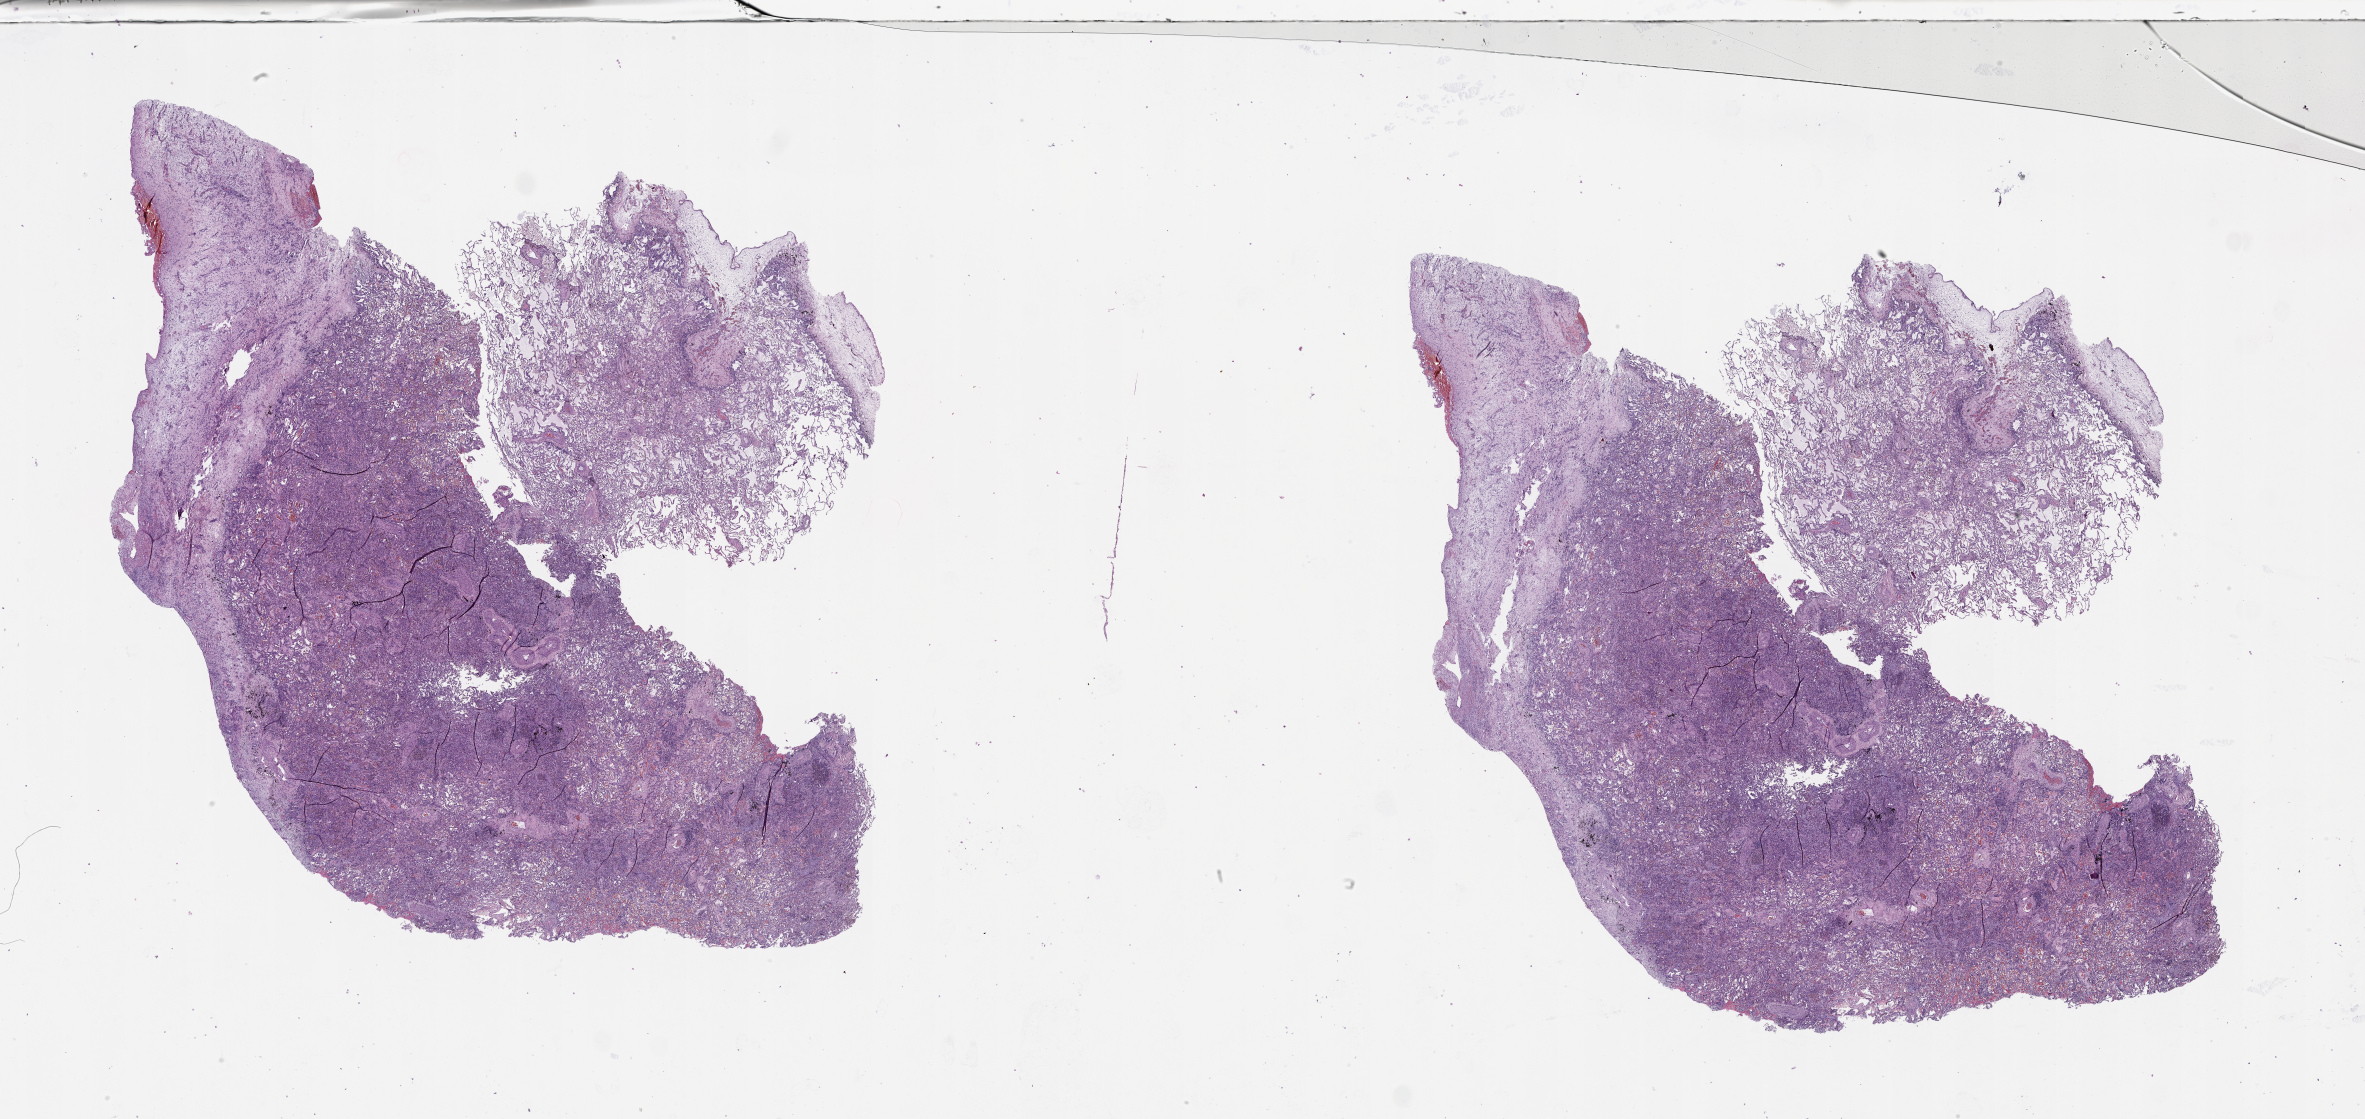
Whole-slide histology image, H&E-stained — a low-resolution overview of the entire scanned area, about 38.1 x 18.0 mm, normal (non-tumour) tissue sample, lung. Male, 57 y/o.
This section: normal (non-tumour) tissue from the same patient. Patient diagnosis (cohort enrolment): squamous cell carcinoma (lung).